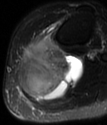
MRI of an extremity soft-tissue mass, one axial slice; T2-weighted fat-saturated; MR volume resampled by the dataset authors to the PET/CT grid (not the native acquisition matrix); 3.27 mm slice thickness; 107 × 125 image matrix, field of view 104 × 122 mm. Female patient. Case-level facts recorded for this patient, not image findings: histological type: extraskeletal high grade osteogenic sarcoma; grade: high; site of the primary tumour: left calf.
Annotated regions visible in this slice (expert contour drawn on MRI and transferred to this co-registered scan by the dataset authors):
- gross tumour volume (mass): bounding box (x1, y1, x2, y2) in pixels: (19, 36, 84, 101)